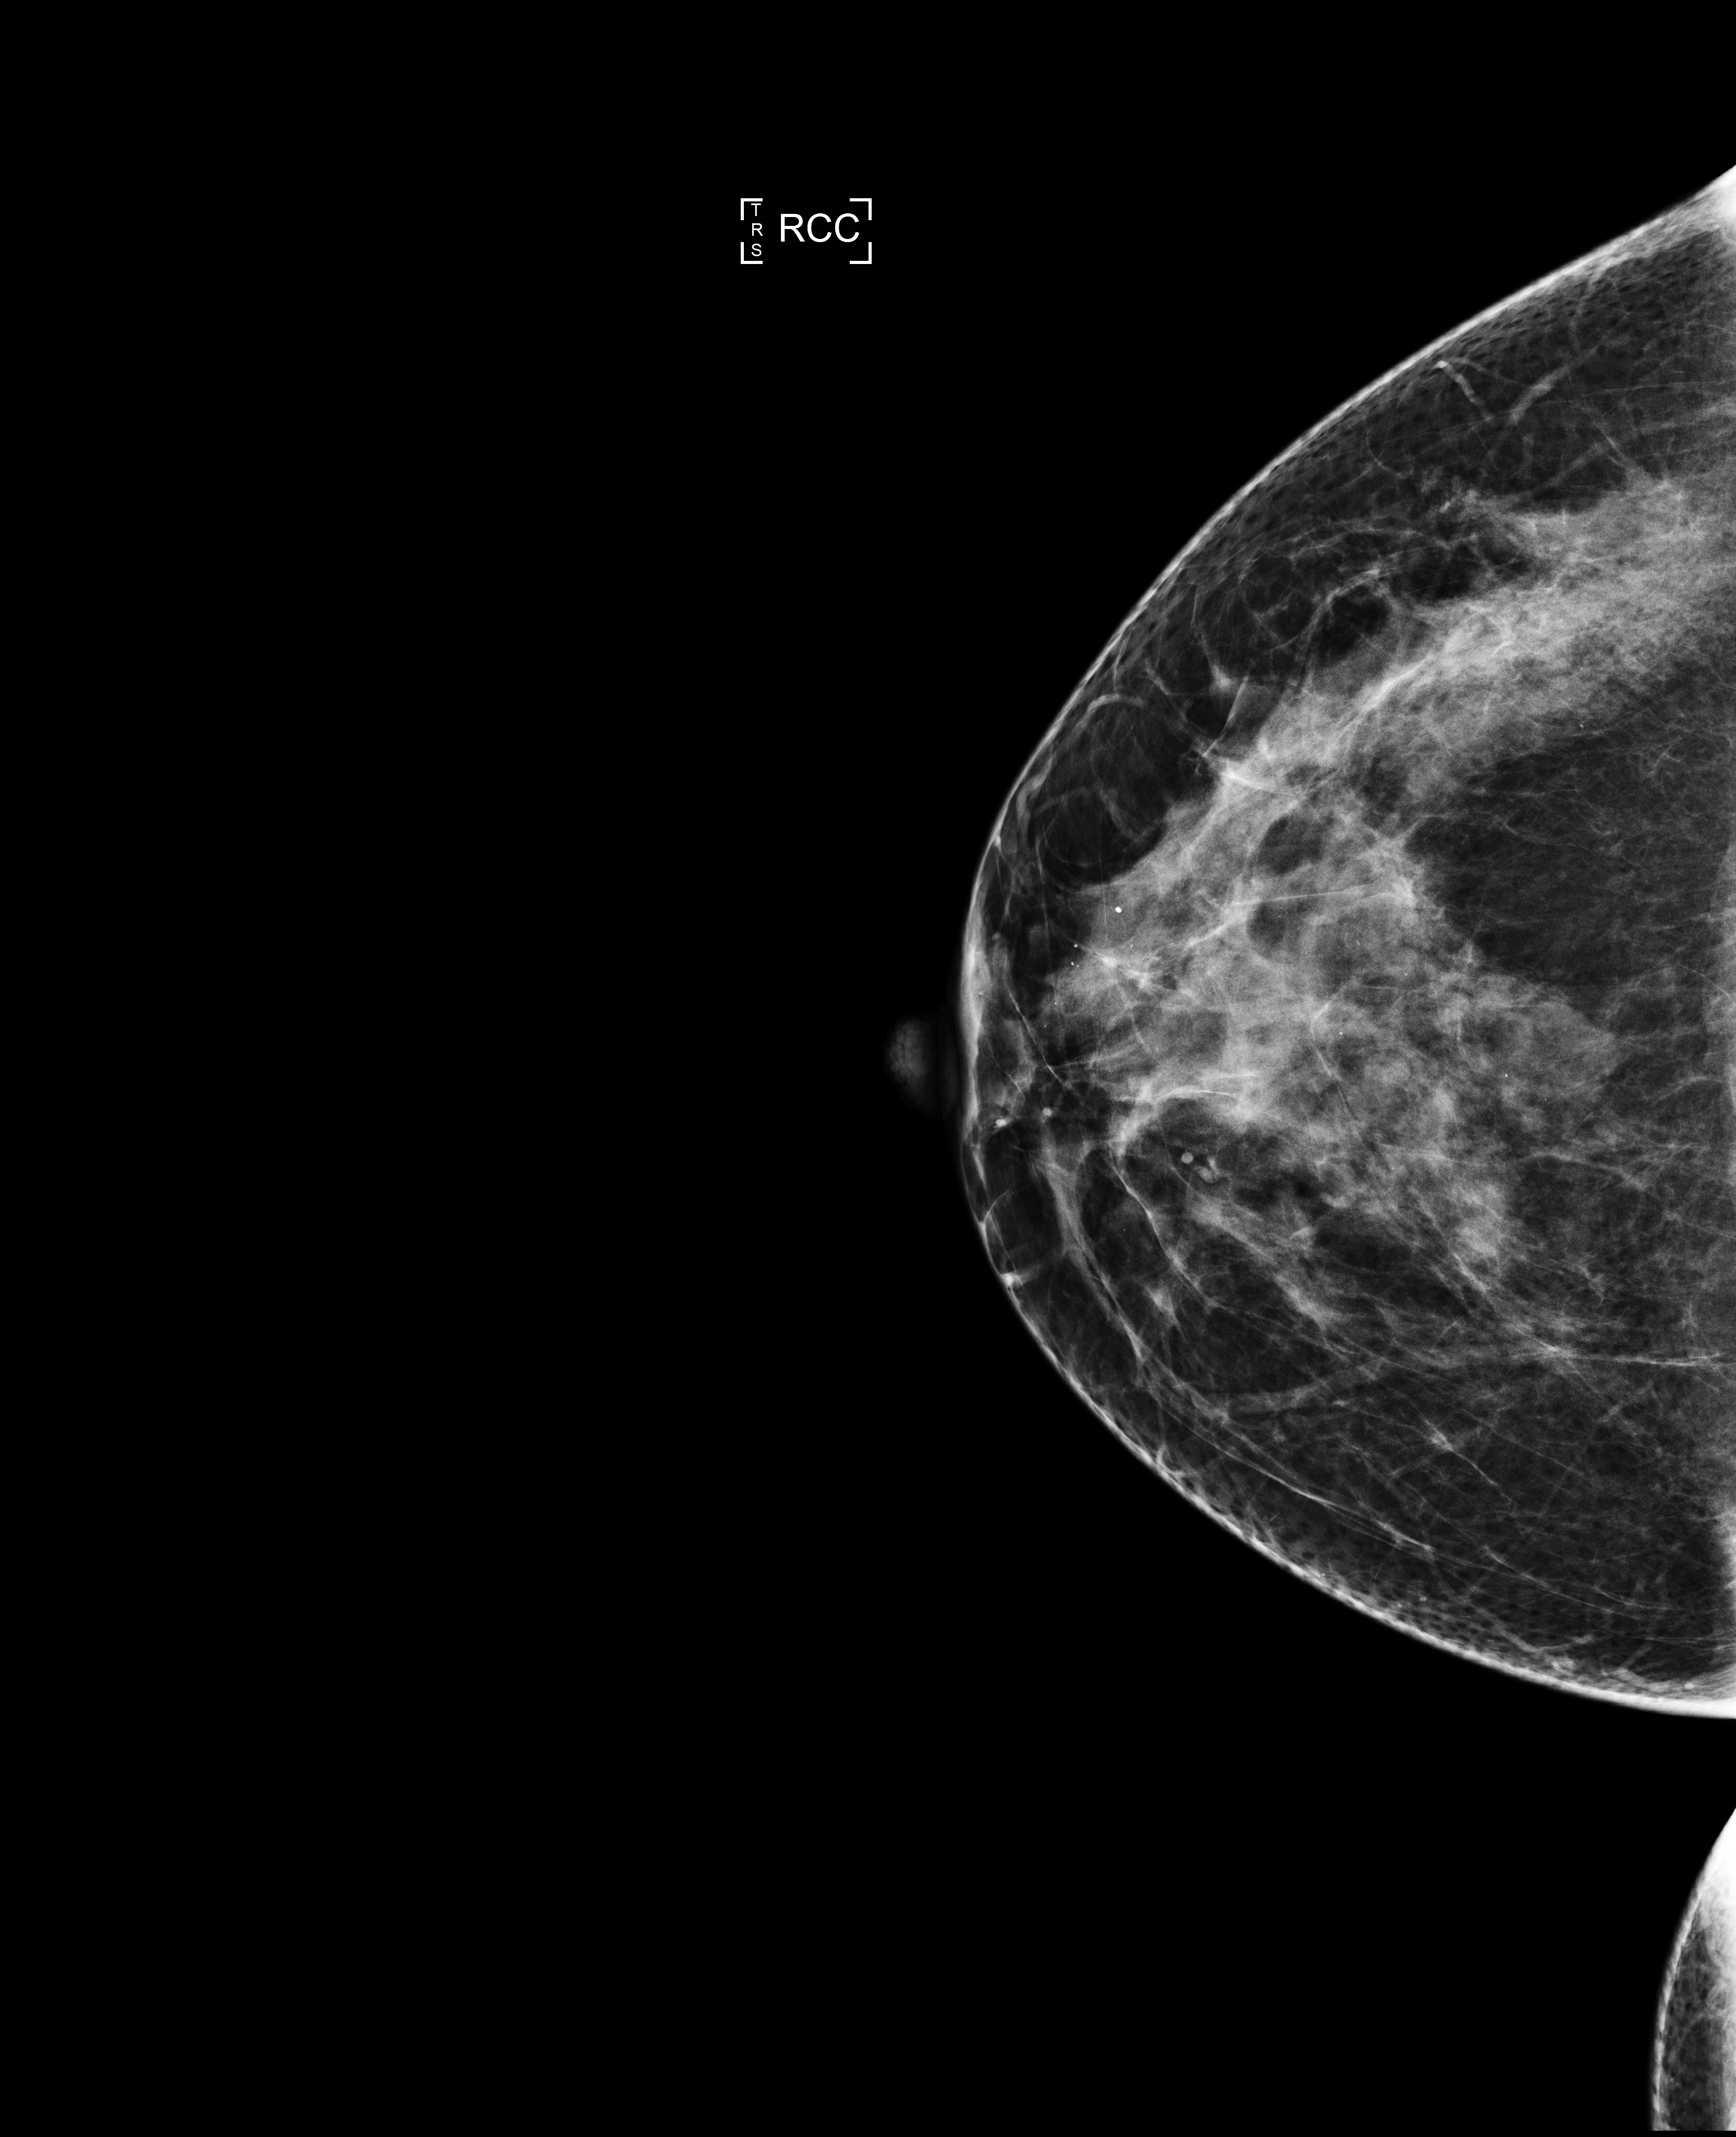
Screening examination; system: Selenia Dimensions. Patient aged 42 years (female).
Image type: full-field digital mammogram. Breast: right. Projection: cranio-caudal projection.